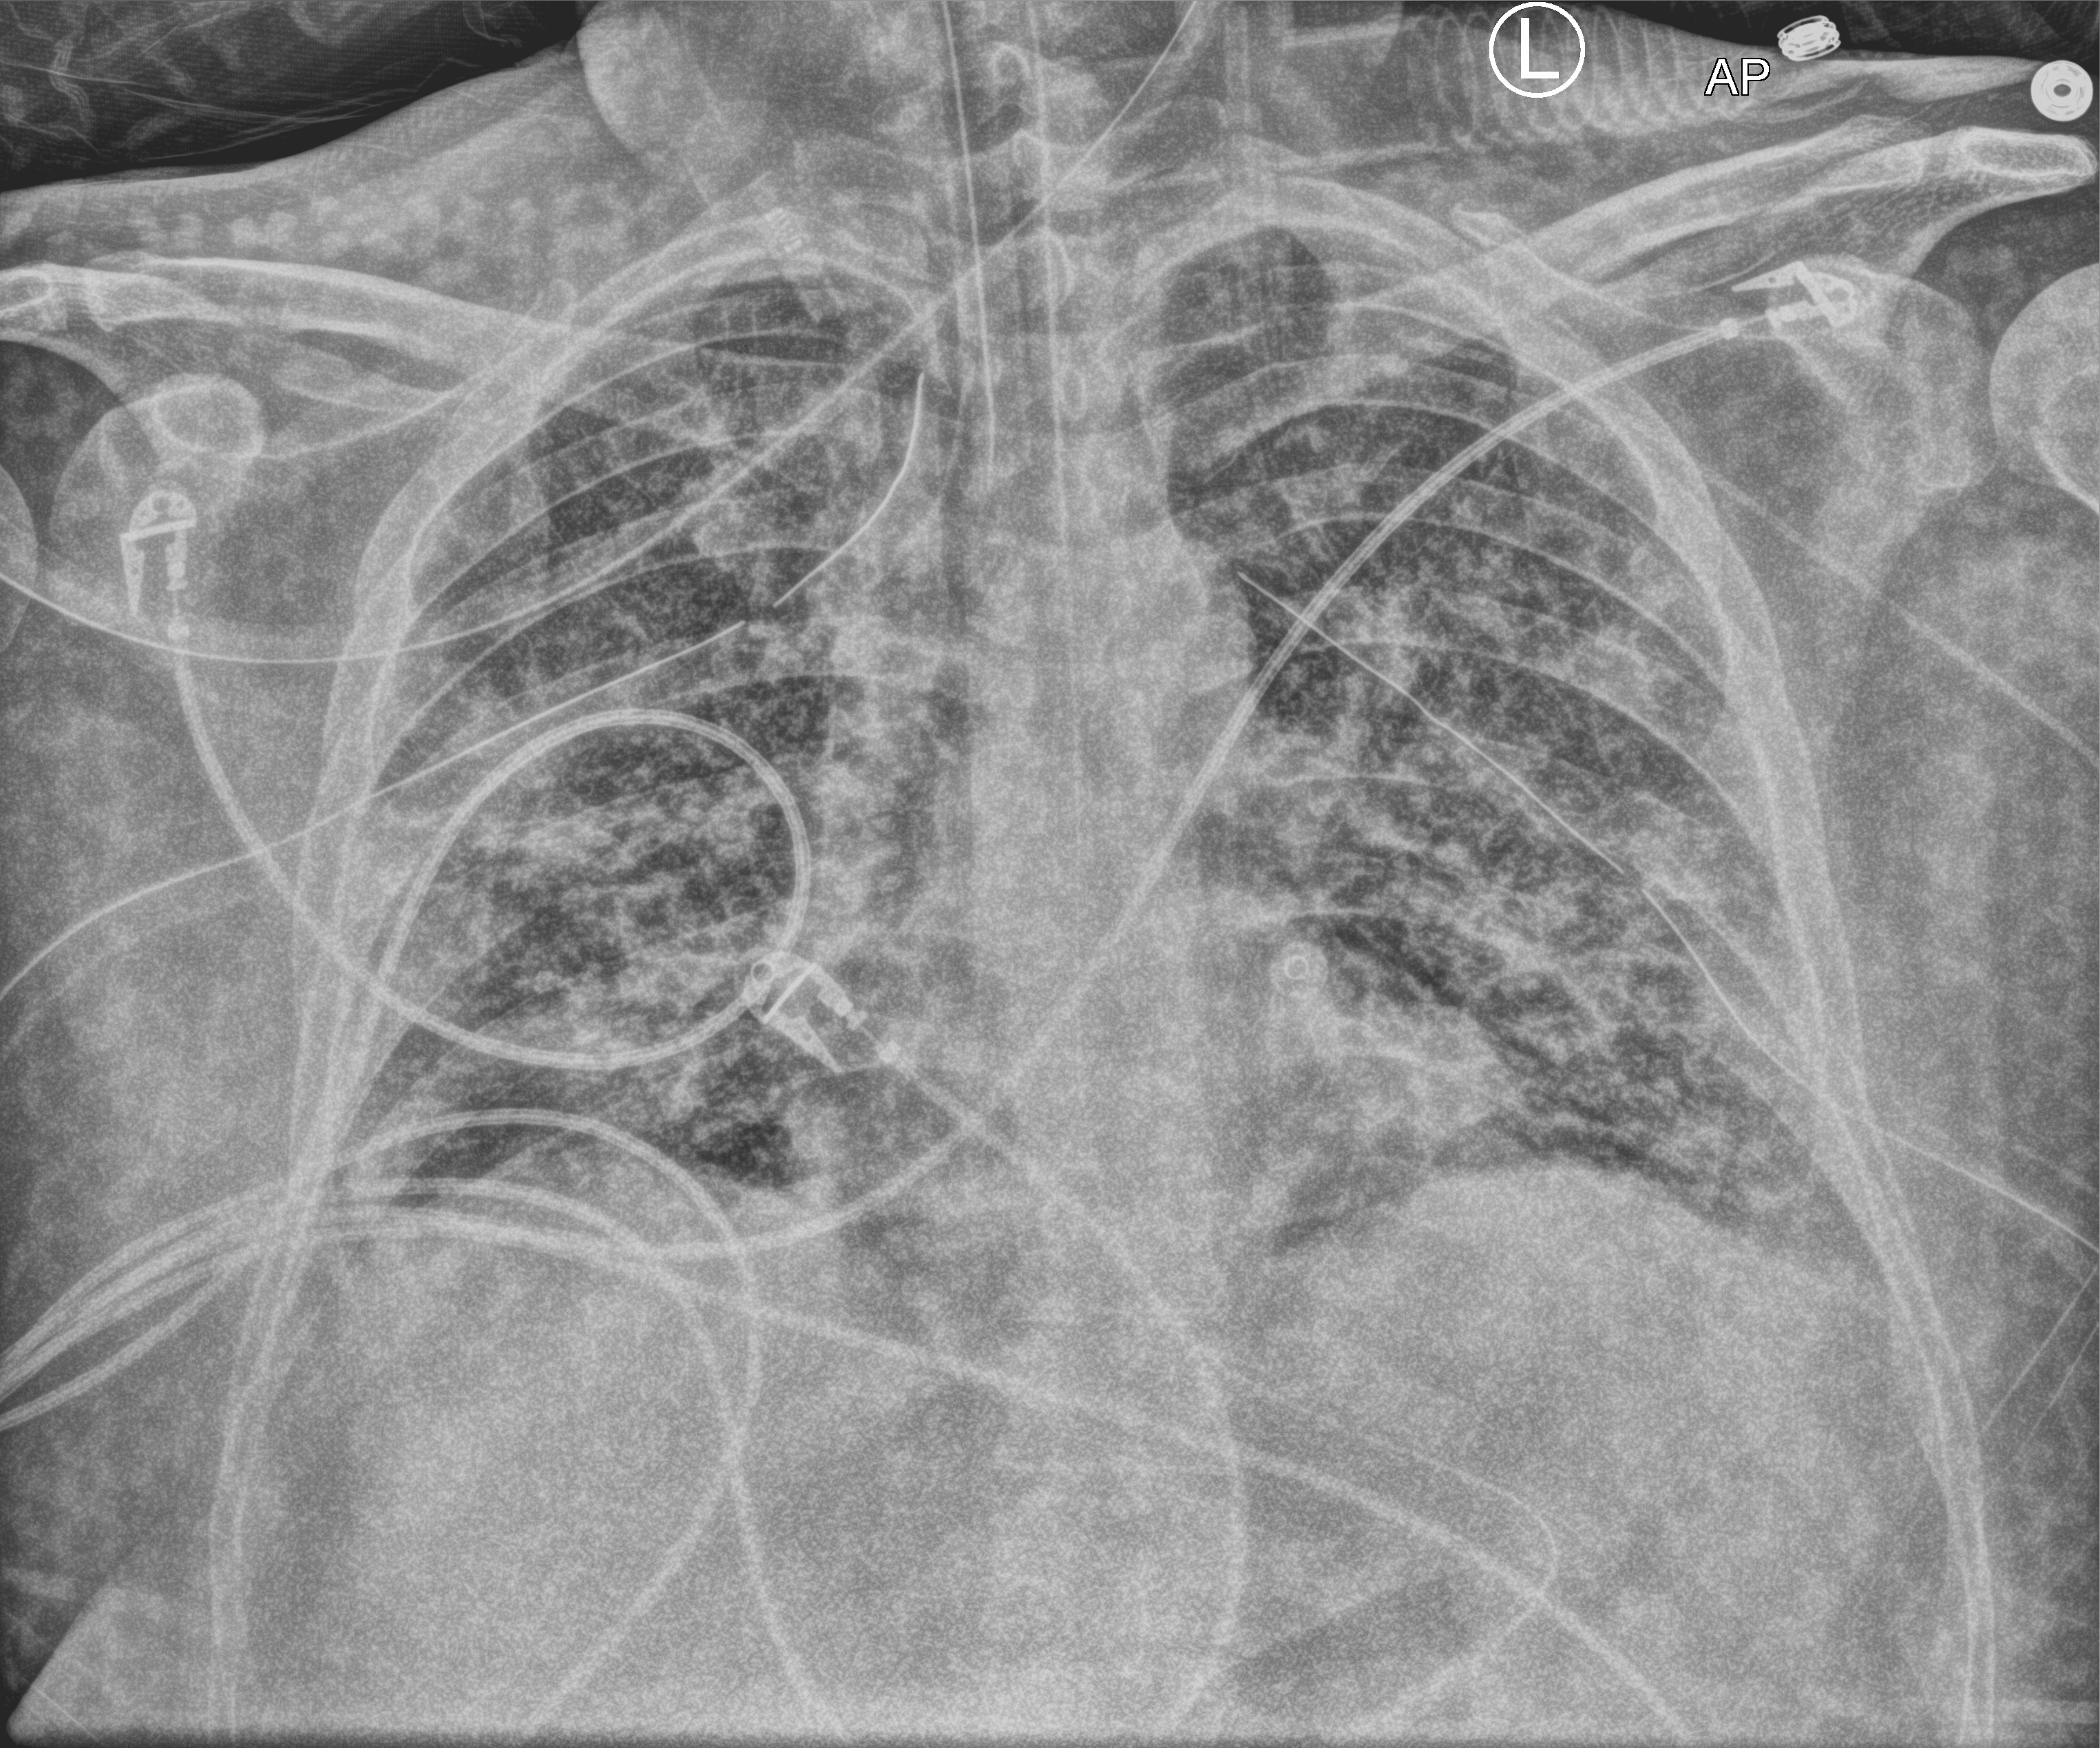
Portable chest radiograph; anteroposterior (AP) projection. Male patient hospitalised with COVID-19, age 18–59 years.
Admission-level facts for this patient (not findings on this image; timing relative to this image not recorded):
- admitted to intensive care during this hospital stay: yes
- chronic kidney disease (admission record): no